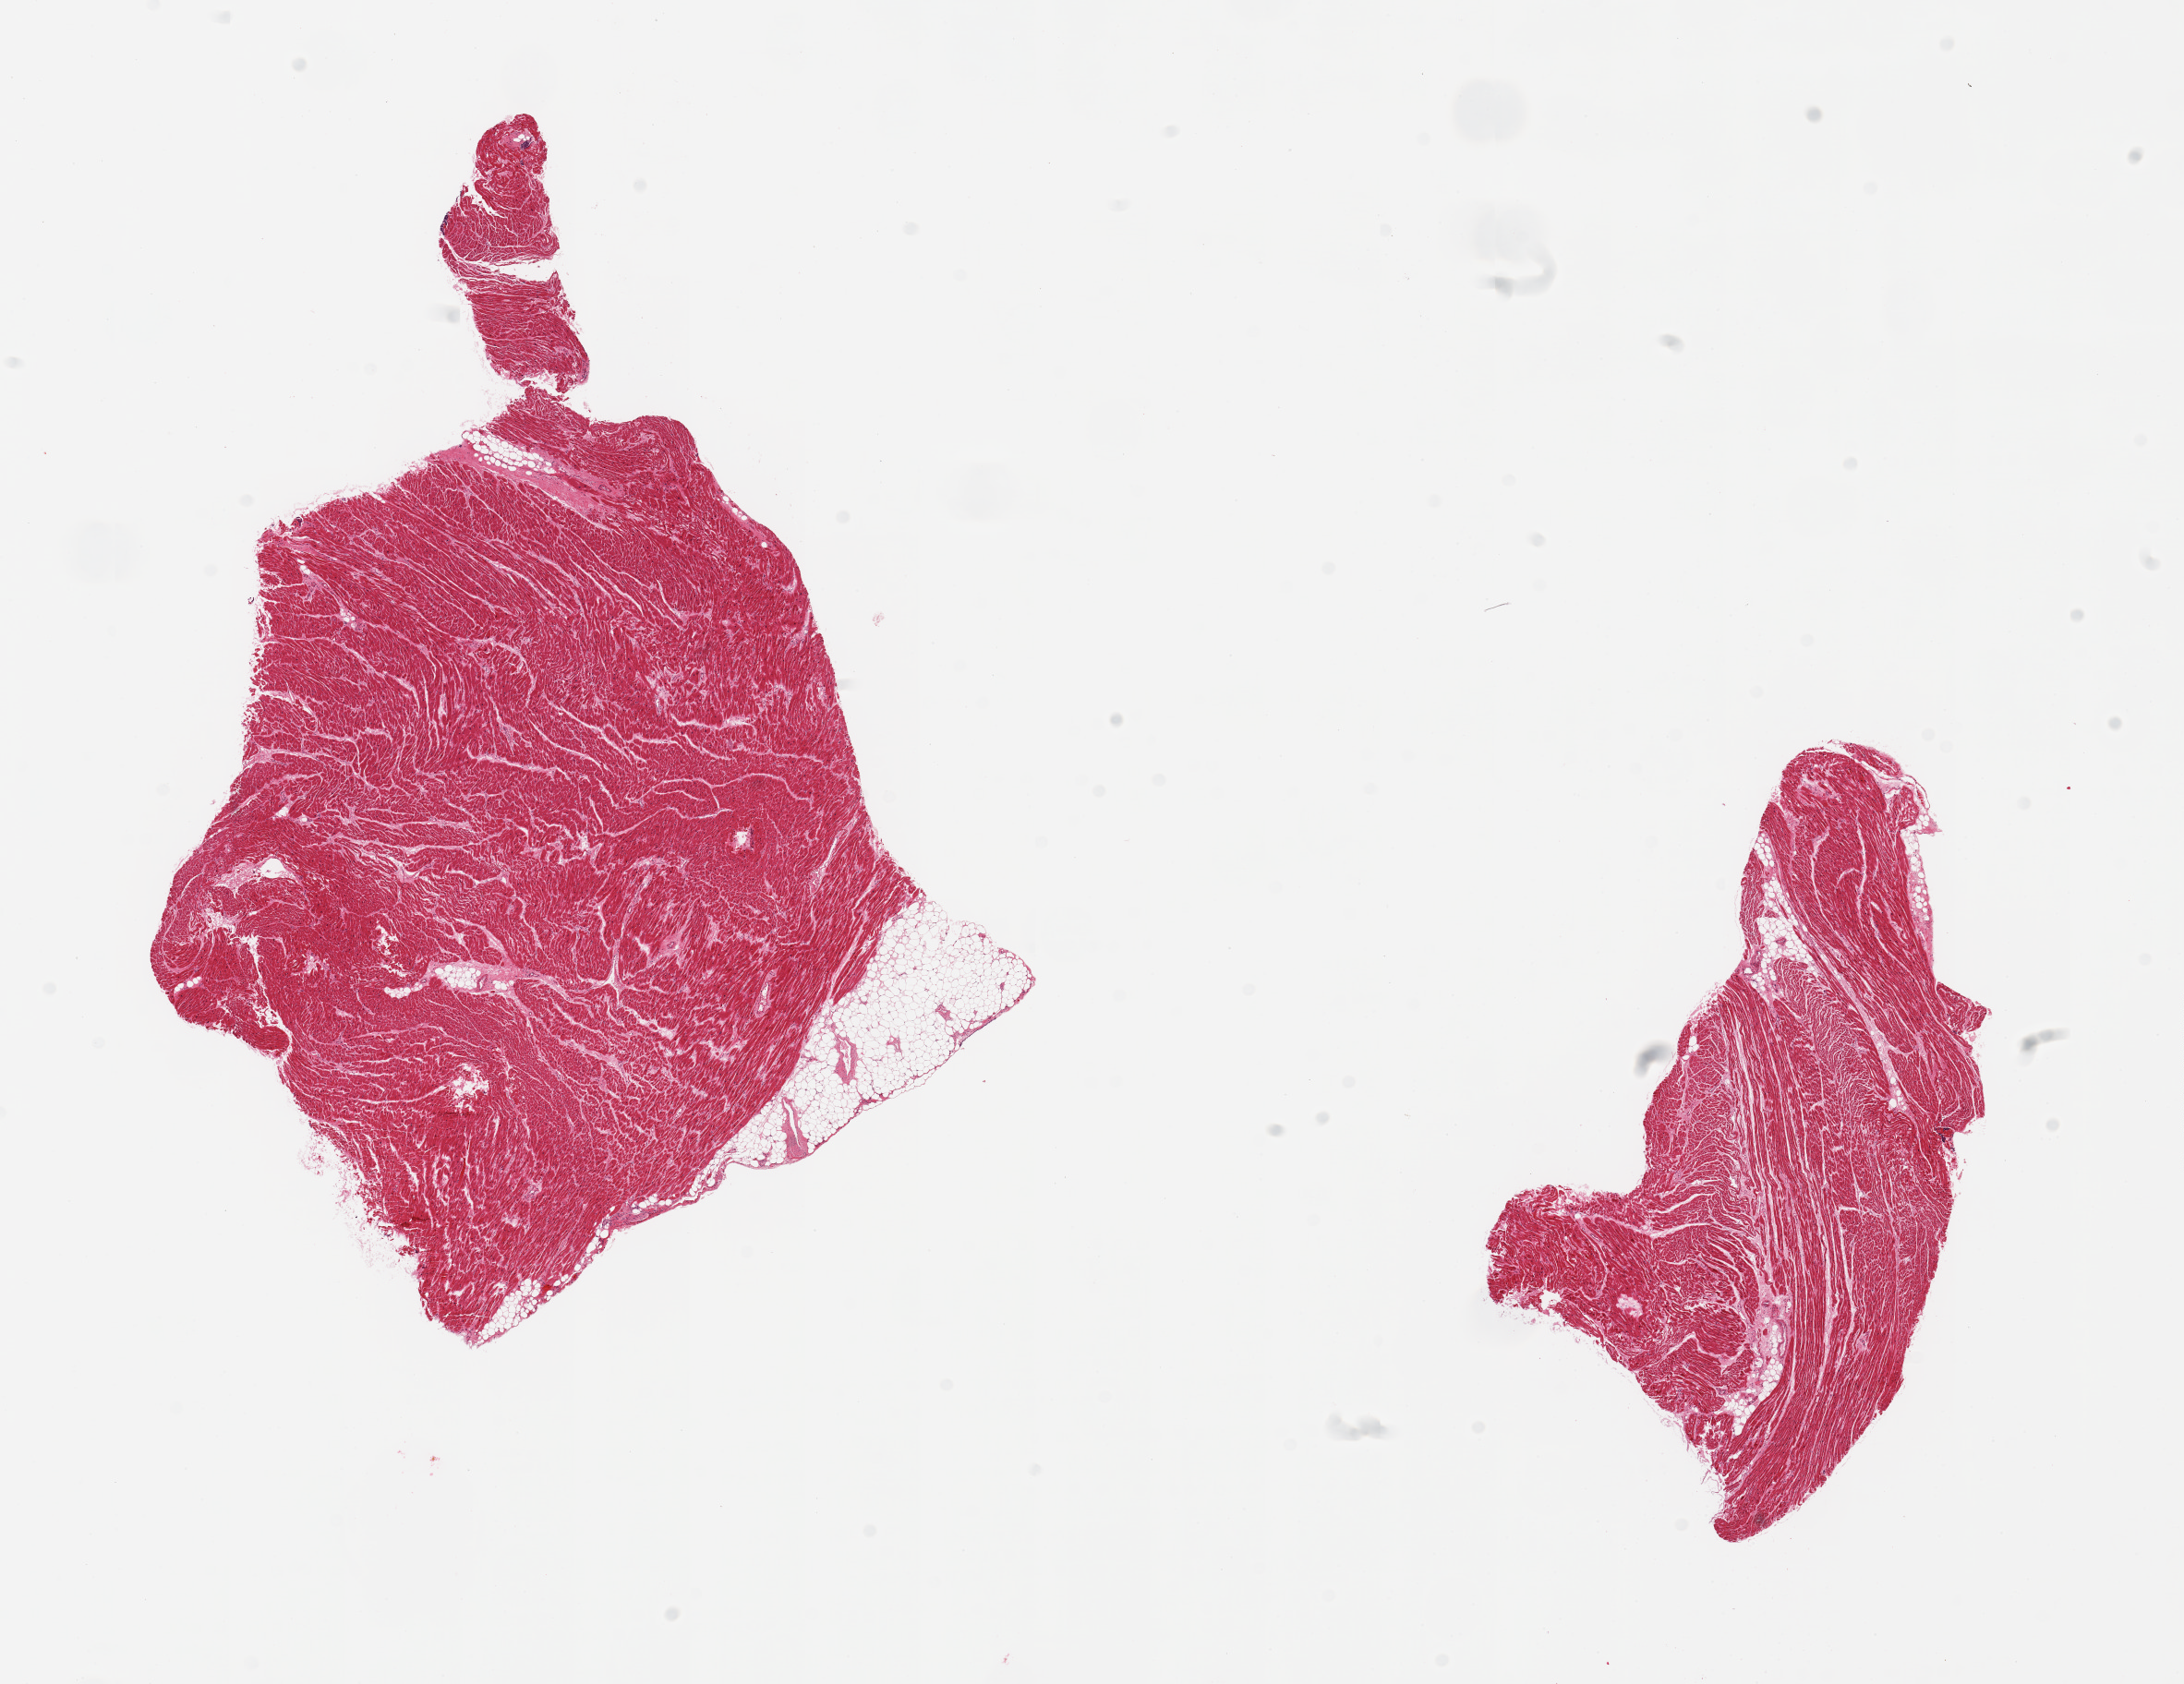
Digitized H&E-stained section, brightfield, a low-resolution overview of the entire scanned area, about 18.7 x 14.4 mm (slide scanned at 20x), PAXgene-fixed, paraffin-embedded tissue, target tissue: heart, donor tissue sample. Male donor.
Reviewer comment on this tissue sample: 2 pieces, minimal interstitial fibrosis, nubbin (1mm) ahderent fat.